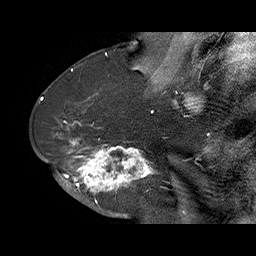
Breast MRI (dynamic contrast-enhanced), one sagittal slice; position 37 of 70 along the scan axis; dynamic contrast-enhanced series, time point 2 of 6 at this slice position (early post-contrast); 1.5 T; TE 4.5 ms, TR 32.4 ms; 256 × 256 image matrix, field of view 180 × 180 mm. Female patient. From the clinical record (not read from this slice): setting: breast cancer imaged before/during neoadjuvant chemotherapy; receptor status: HR-positive, HER2-negative.
Structures marked on this image (semi-automatically segmented with operator editing):
- analysis volume of interest (the breast-tissue region the enhancement analysis was run in; not a lesion): bounding box <71,128,159,202> (left, top, right, bottom; pixels)
- tumour enhancement mask (voxels above the 100 % enhancement threshold inside the analysis volume of interest): <71,138,156,202>